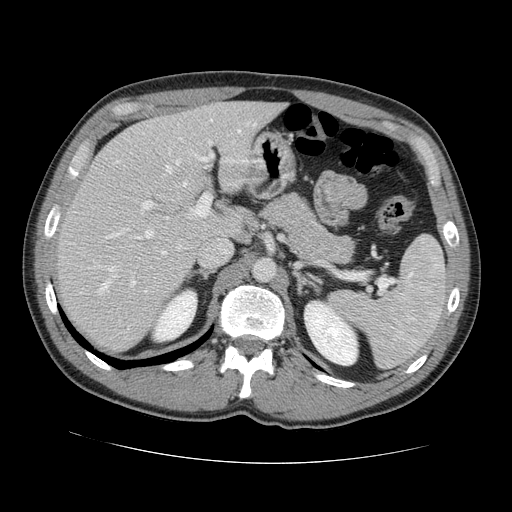
Contrast-enhanced abdominal CT, one axial slice. Slice 87 of 131 in the series (ordered by position). 120 kVp. Intravenous contrast given. Soft-tissue window (W 400 / L 40 HU). 2.5 mm slice thickness. 512 × 512 image matrix. Male patient, age 40 years. From the clinical record (not read from this slice): diagnosis: colorectal cancer liver metastases, imaged before liver resection; multiple liver metastases: yes; largest metastasis: 2.9 cm; disease in both lobes: yes.
Structures marked on this image (outlined manually by an expert reader):
- hepatic veins: bounding box (x1, y1, x2, y2) in pixels: (97, 158, 187, 293)
- liver: (60, 103, 280, 351)
- planned liver remnant (the part of the liver to remain after resection): (102, 103, 281, 237)
- portal vein (with intrahepatic branches): (105, 154, 213, 287)